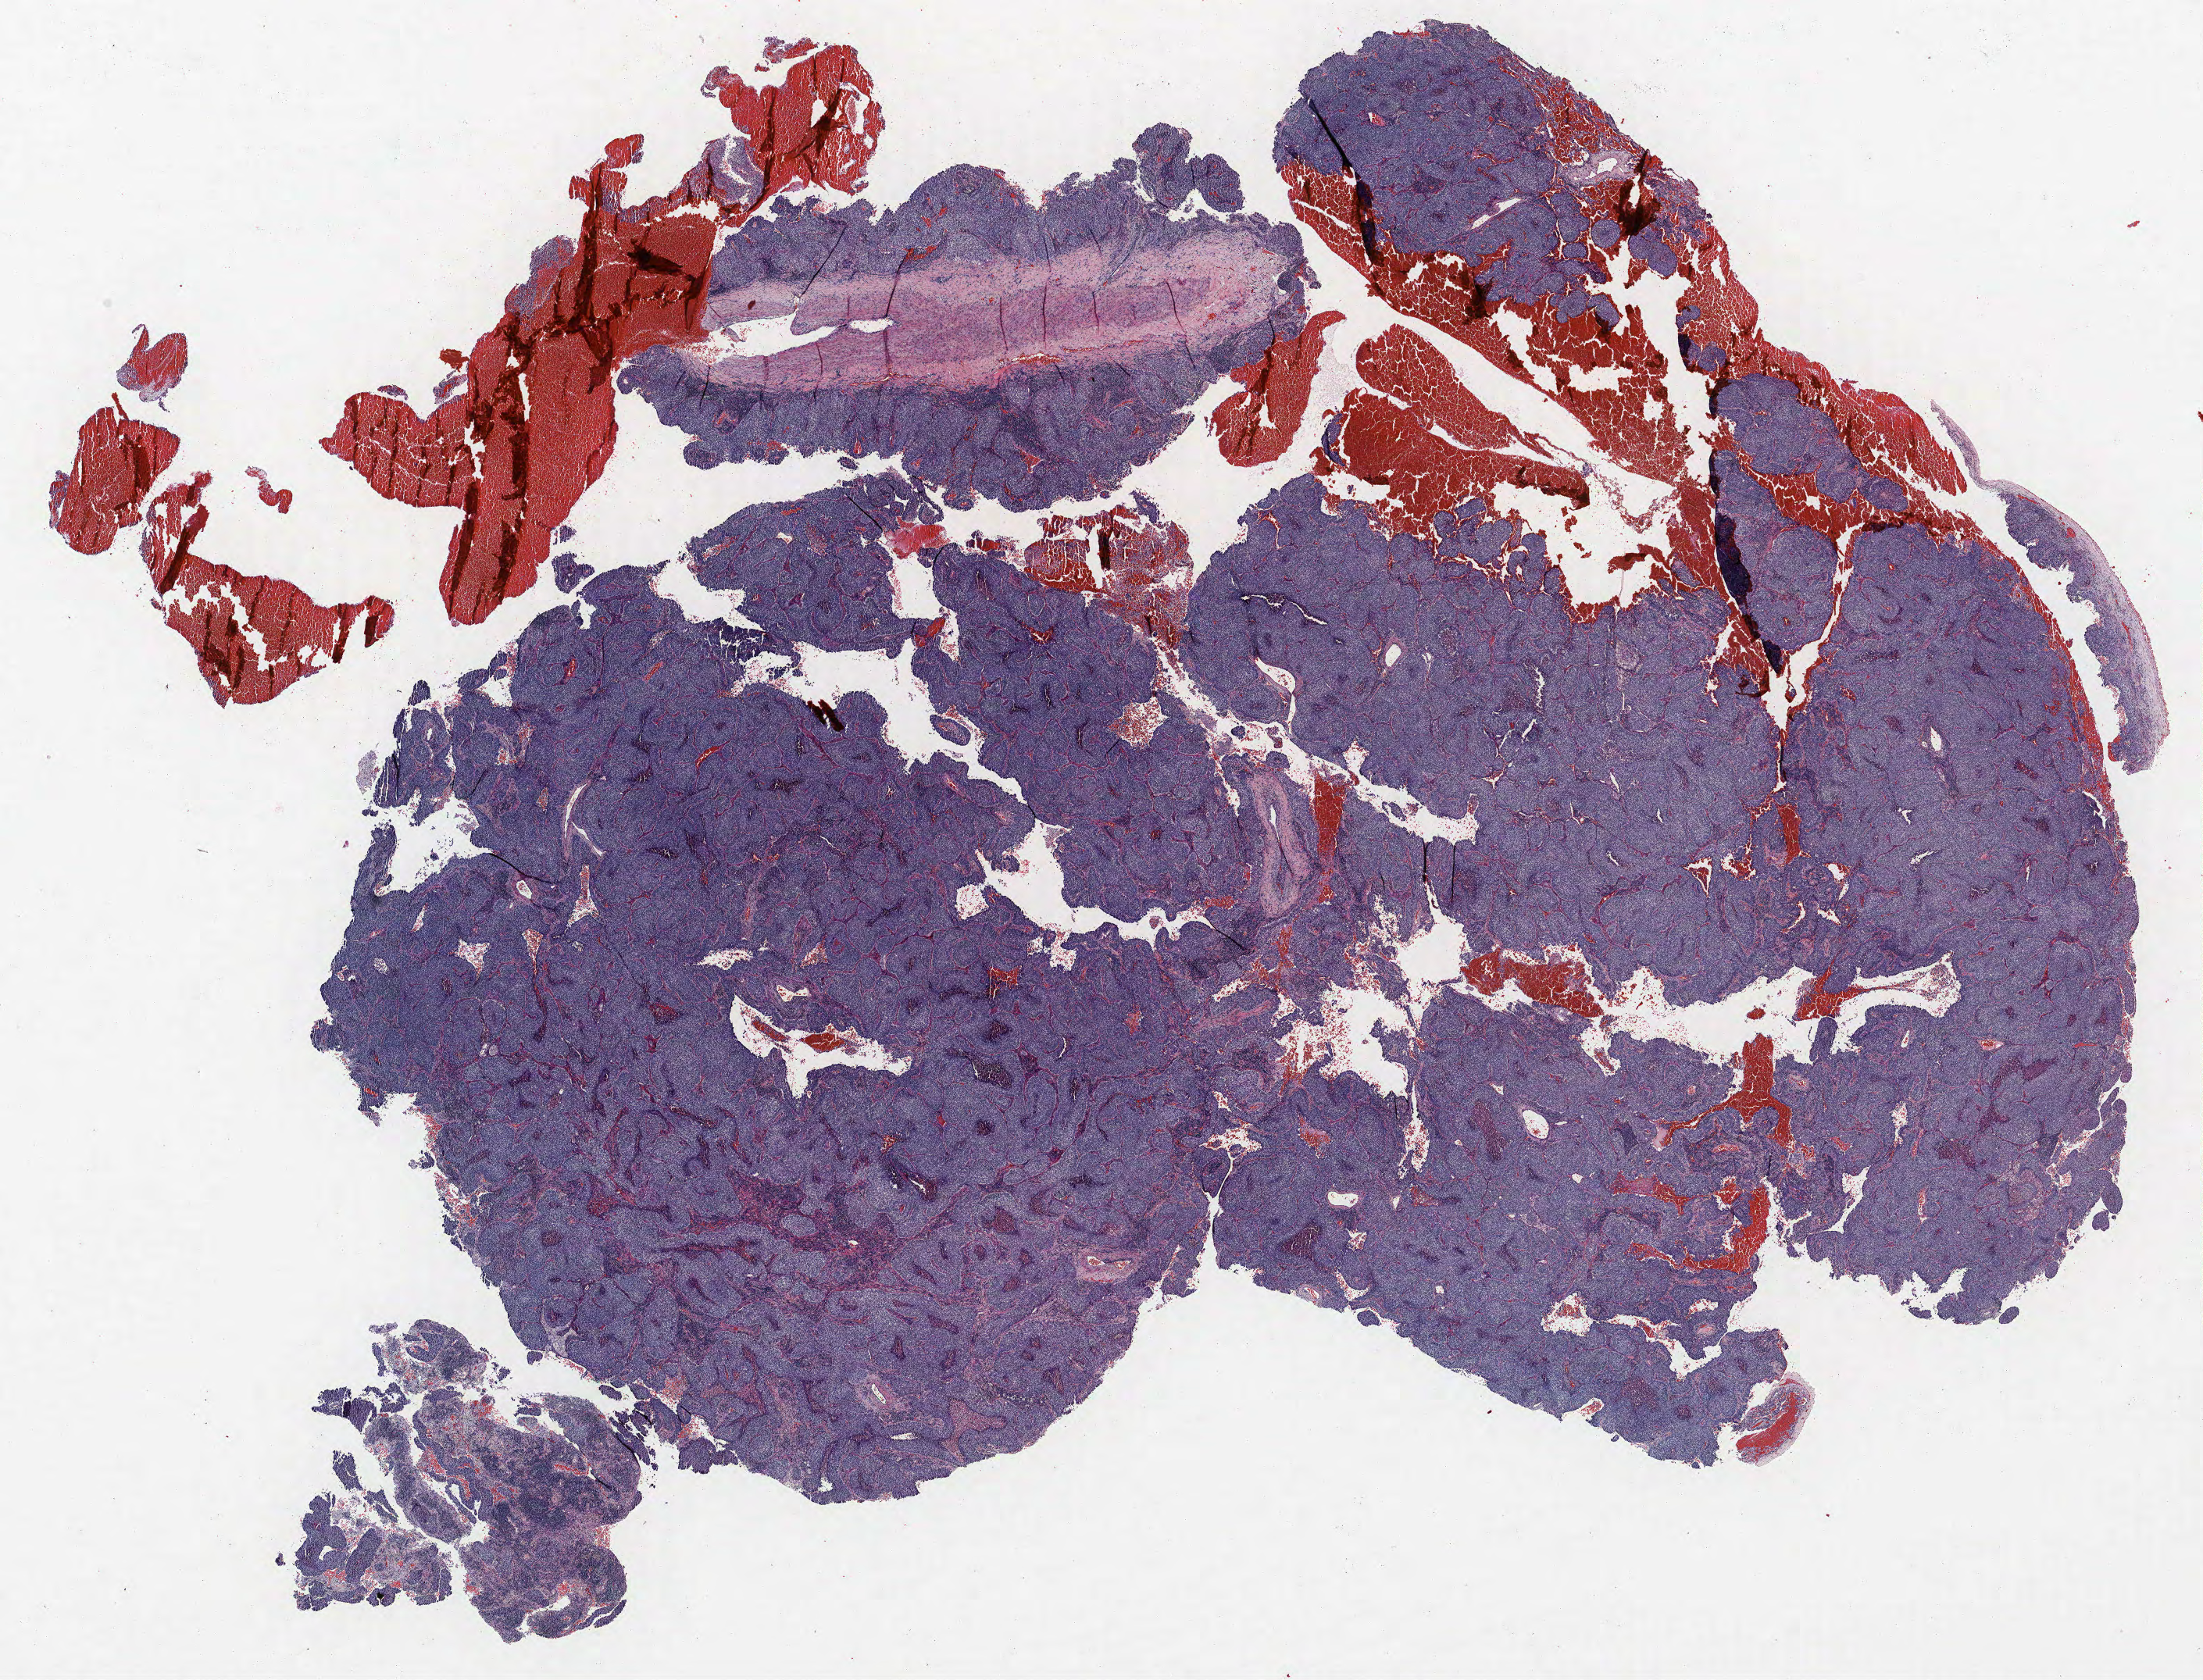
Whole-slide histology image, H&E-stained, shown as a low-resolution overview of the whole scanned area (about 22.6 x 17.2 mm, slide scanned at 40x). FFPE section. Lung. Male patient, aged 65 at enrolment. Former smoker at enrolment. Grade: moderately differentiated (G2).
Participant's lung-cancer diagnosis: Adenocarcinoma, NOS (ICD-O-3 8140/3). Tumour size (pathology): 25 mm. Stage (AJCC 6th edition): IA. Primary tumour location (clinical record): right middle lobe.